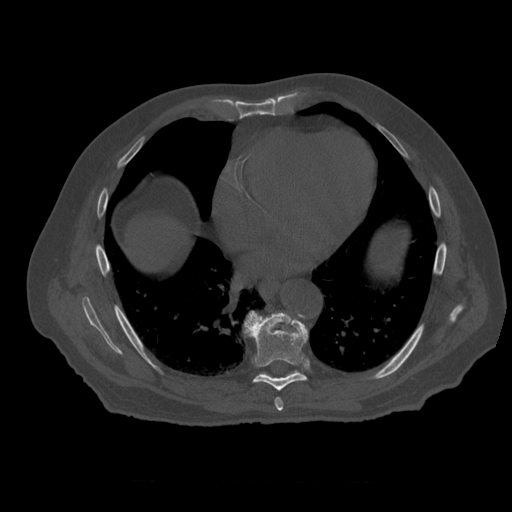
CT including the spine, one axial slice; position 339 of 399 along the scan axis; reconstruction kernel STANDARD; 120 kVp; bone window (W 1800 / L 400 HU); 512 × 512 image matrix, field of view 407 × 407 mm. Patient age 73 years. From the clinical record (not read from this slice): primary cancer: prostate.
Outlined on this slice (semi-automatically segmented with operator editing):
- T7 vertebra: bounding box <275,398,283,413> (left, top, right, bottom; pixels)
- T8 vertebra: <244,312,309,391>
- T9 vertebra: <250,311,298,378>